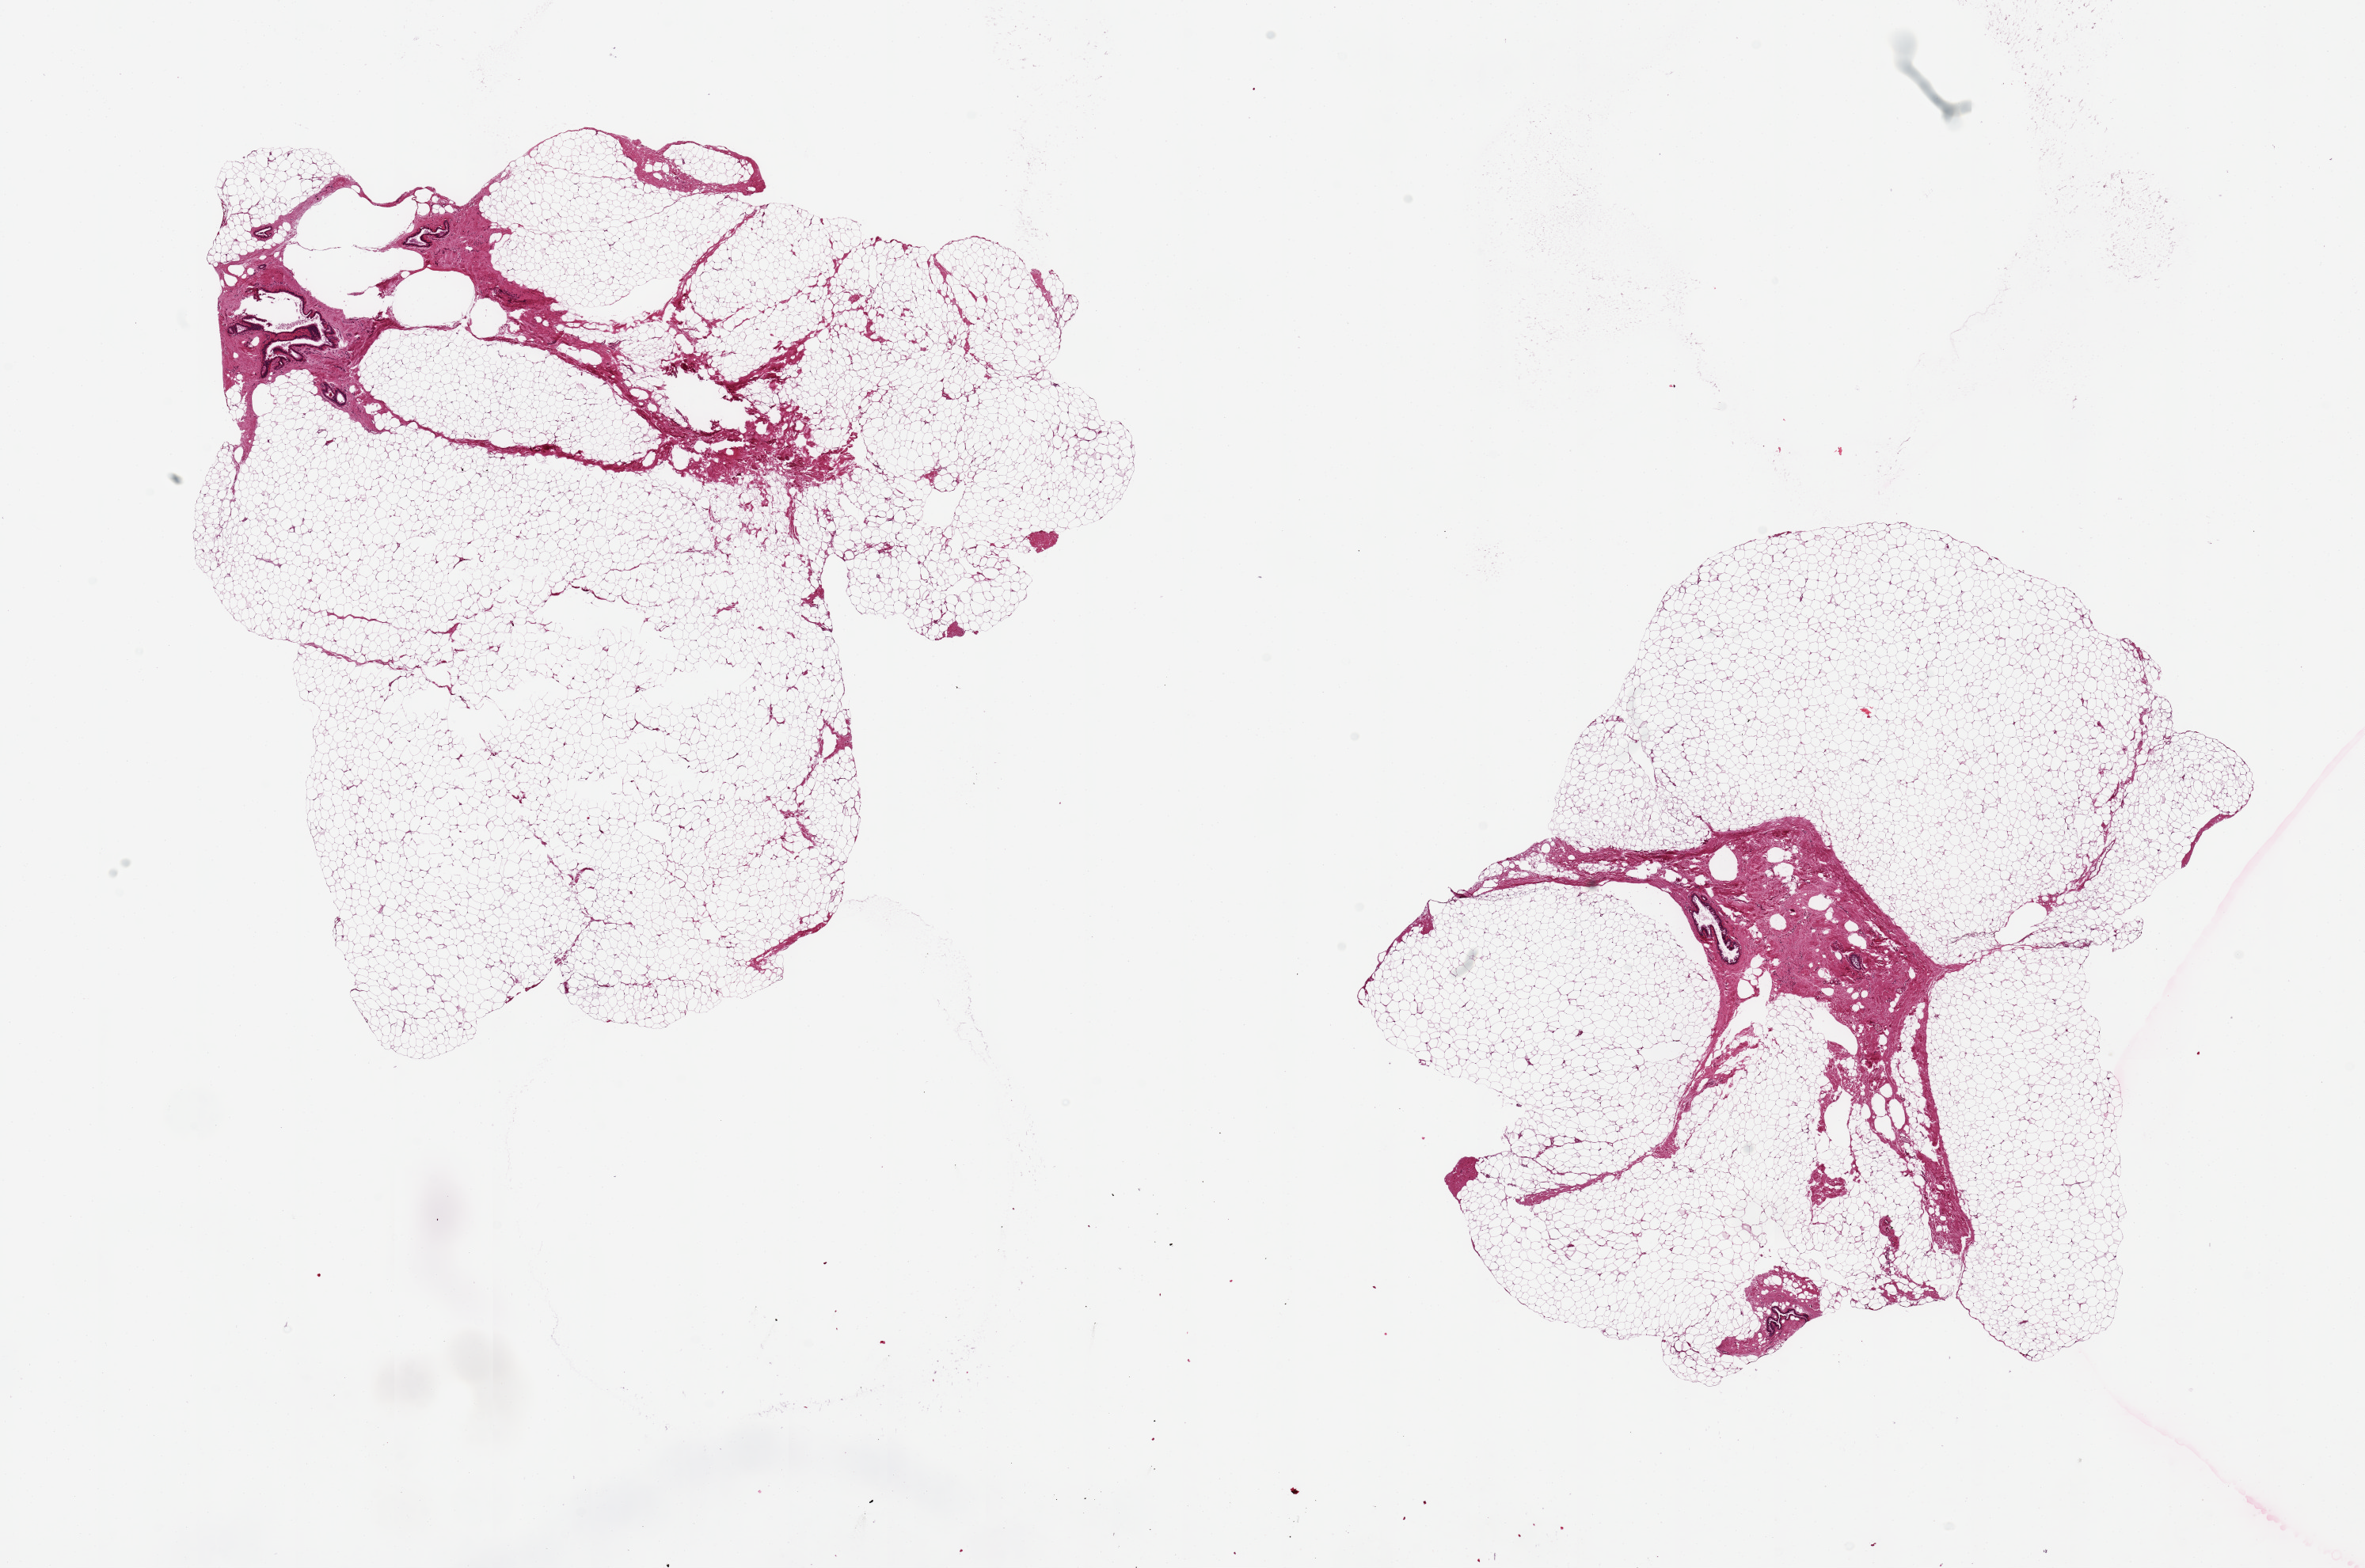
Haematoxylin and eosin whole-slide image, low-resolution overview of the scanned area, about 23.6 x 15.7 mm (acquisition: 20x scan). PAXgene-fixed, paraffin-embedded tissue. Target tissue: breast. Donor tissue sample.
Reviewer comment on this tissue sample: 2 pieces 9x9 & 8x7 mm; several foci of mammary ducts in abundant fibroadipose tissue.